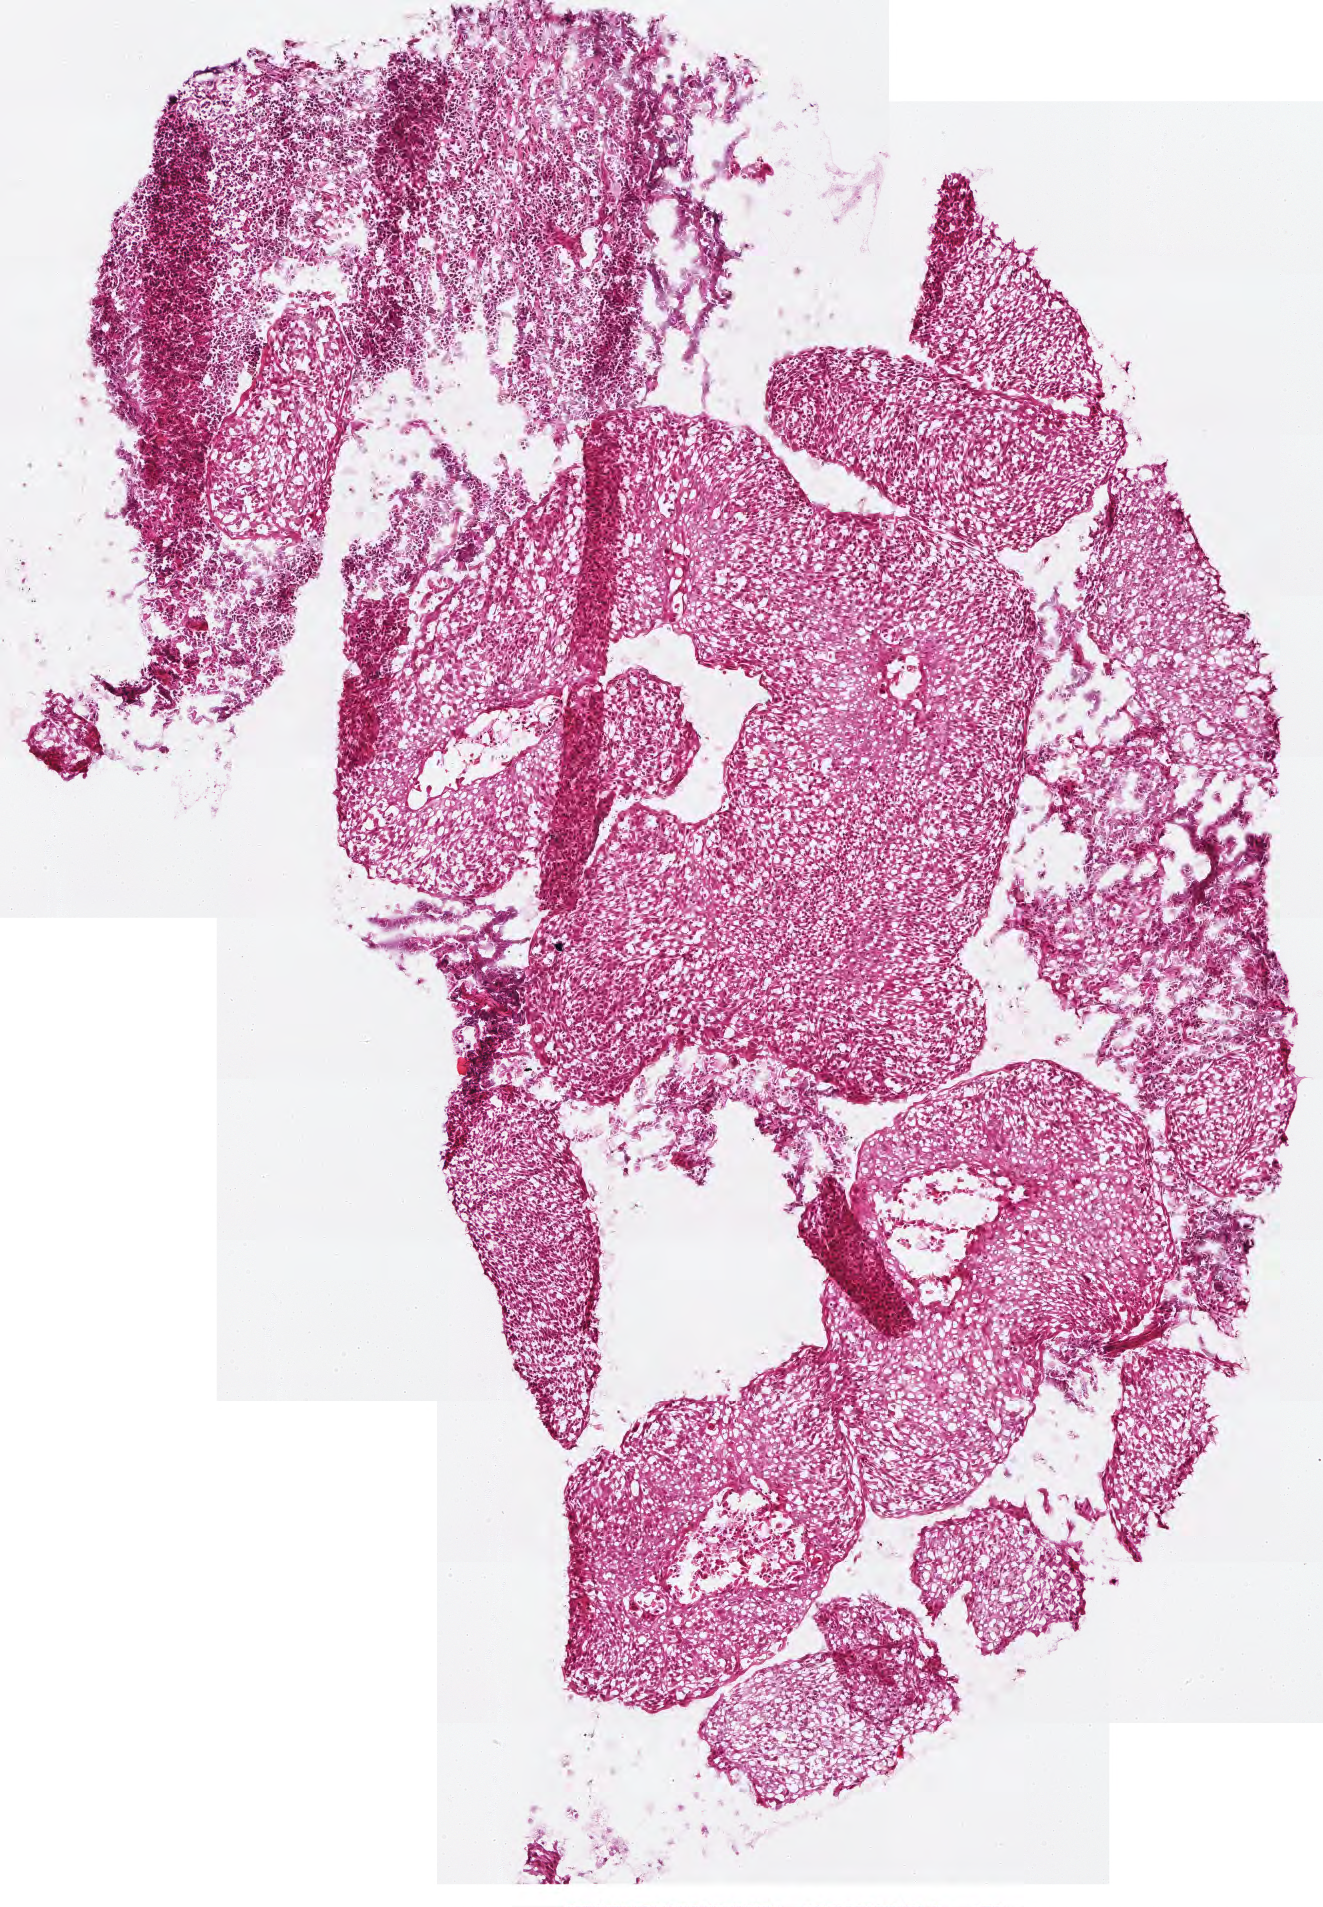
Whole-slide histology image, H&E — shown as a low-resolution overview of the whole scanned area (about 2.6 x 3.8 mm). Frozen section from the top of the tissue portion. Sample: primary tumour, head and neck. Male, age 47 years at initial diagnosis. Histologic grade: G2 (moderately differentiated). Composition of this section per pathologist review: tumour cells 95%, tumour nuclei 90%, normal cells 0%, stromal cells 5%, necrosis 0%.
Laterality: right. Diagnosis: Squamous cell carcinoma, NOS (tonsil, NOS).